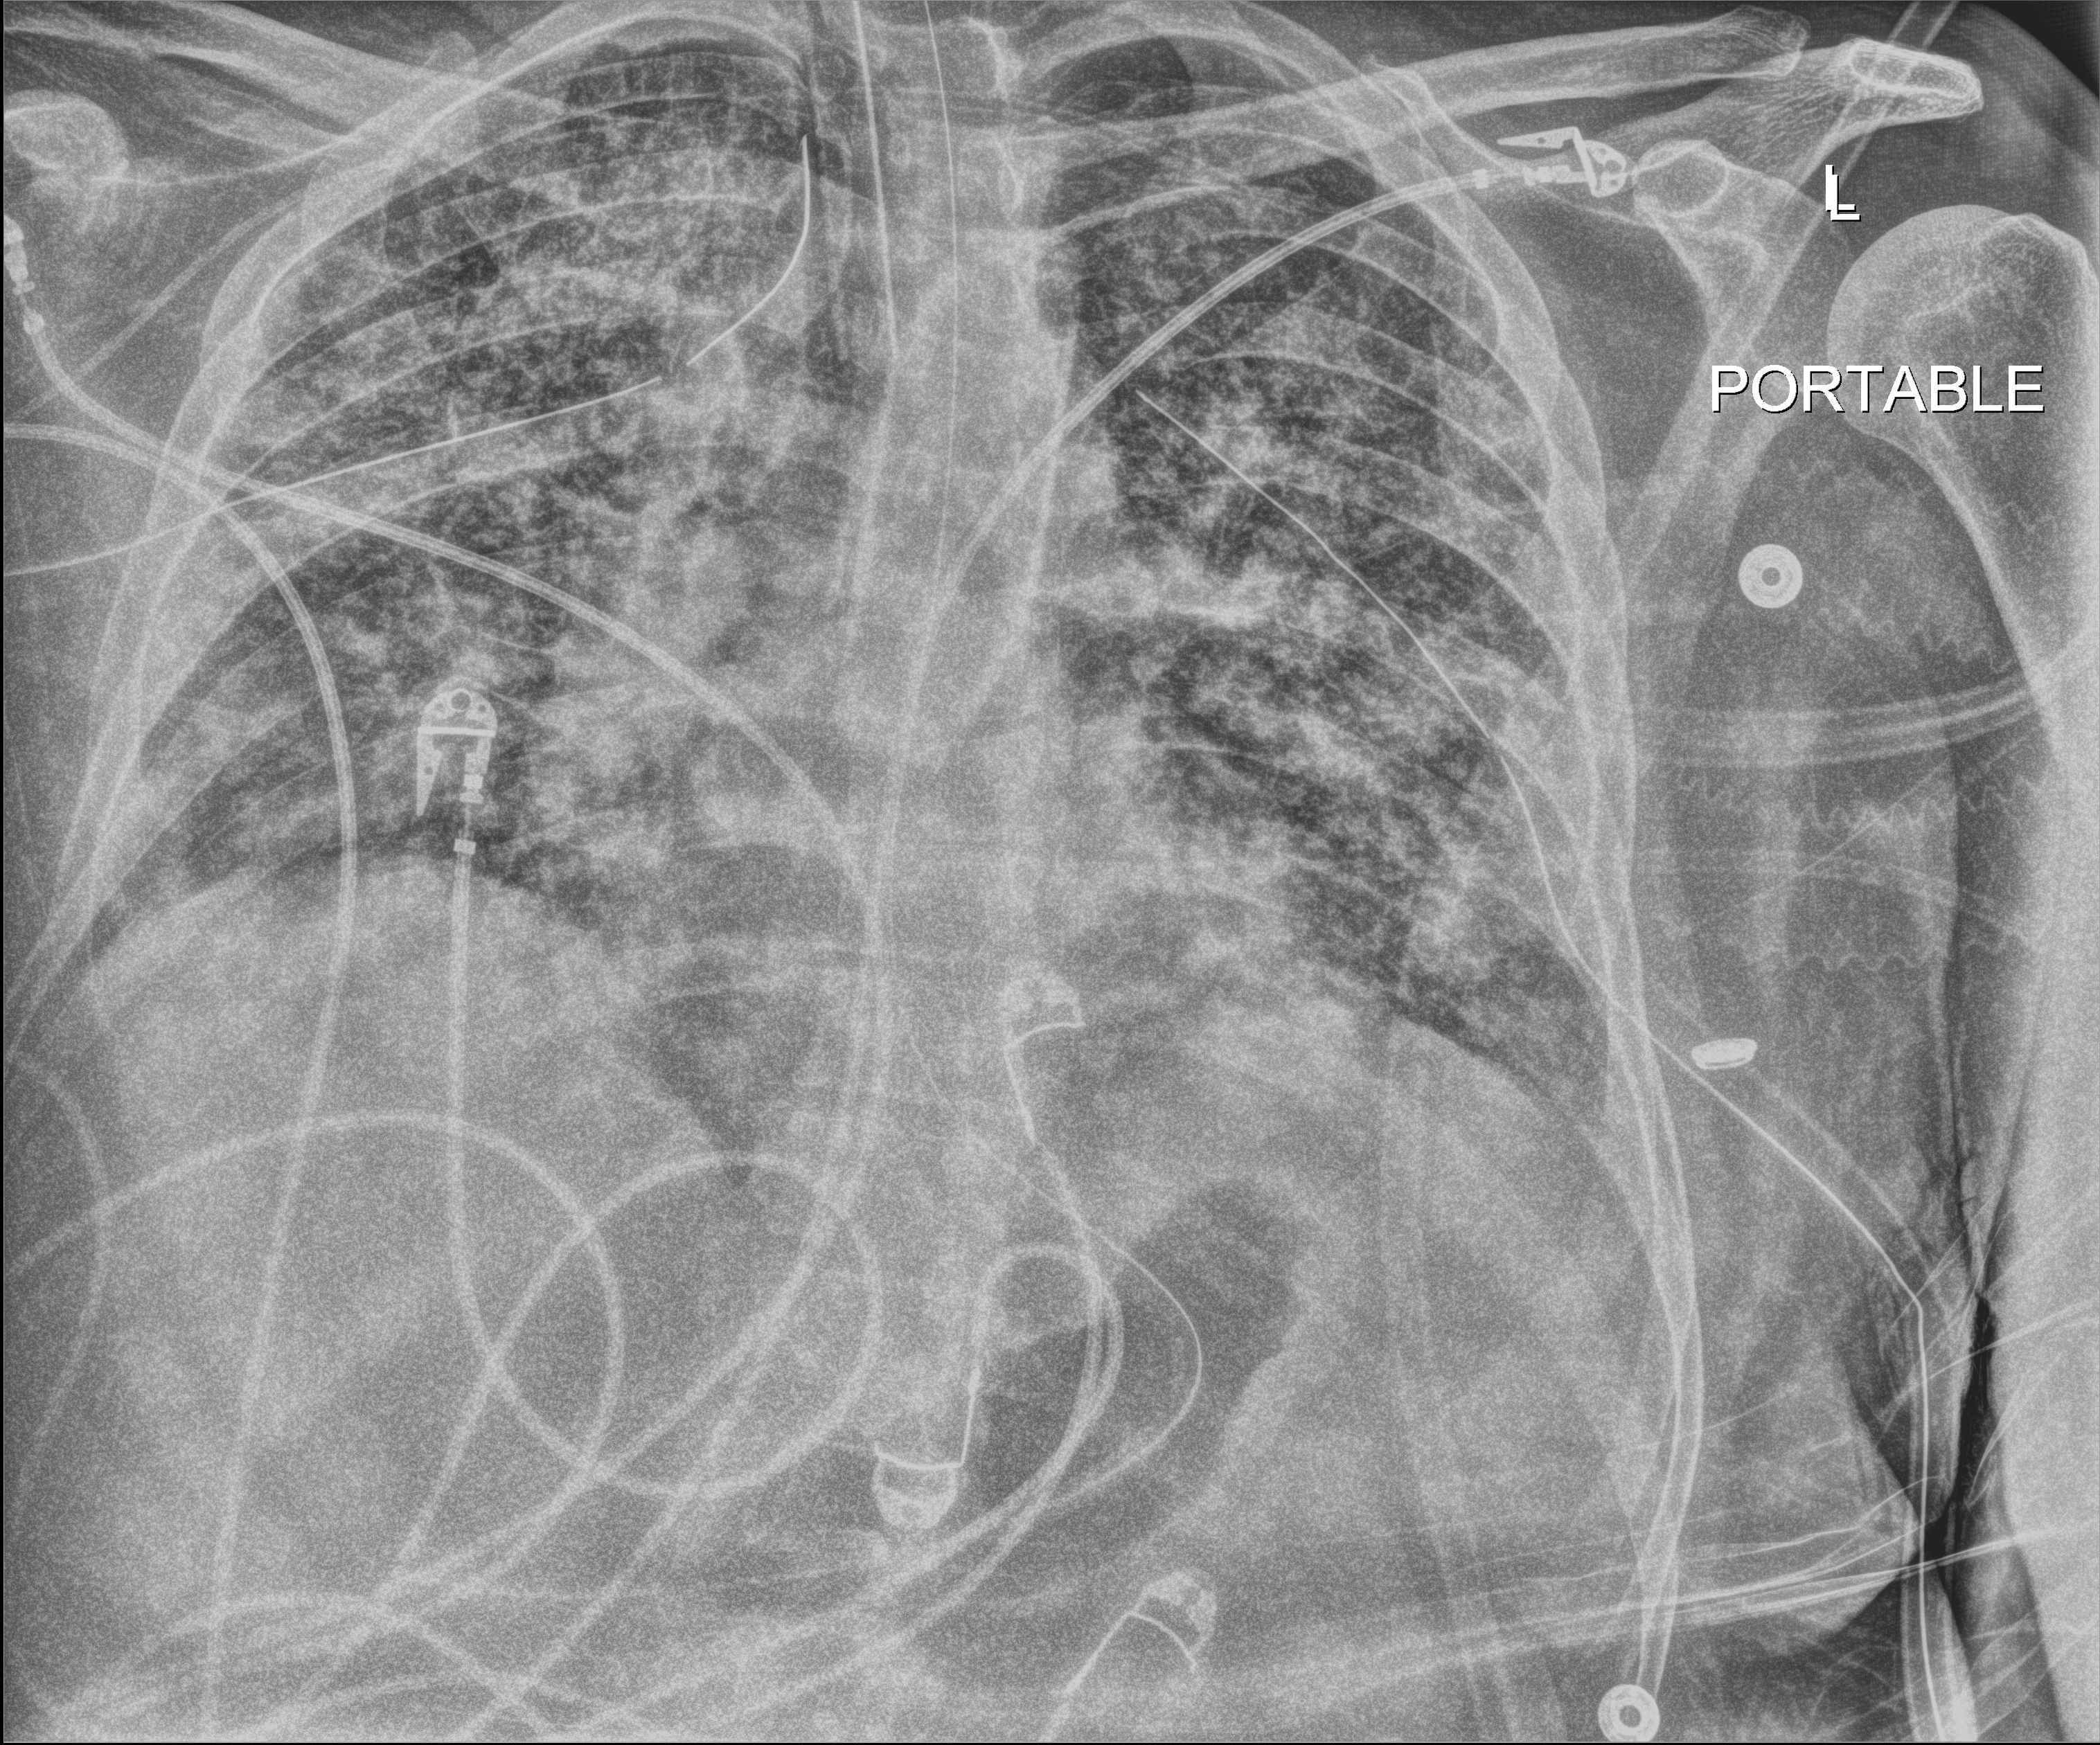
Chest radiograph (digital radiography). Male patient hospitalised with COVID-19, age 18–59 years.
Hospital-stay facts (about this admission, not read from this image; timing relative to this image not recorded): length of hospital stay: 63 days; admitted to intensive care during this hospital stay: yes.